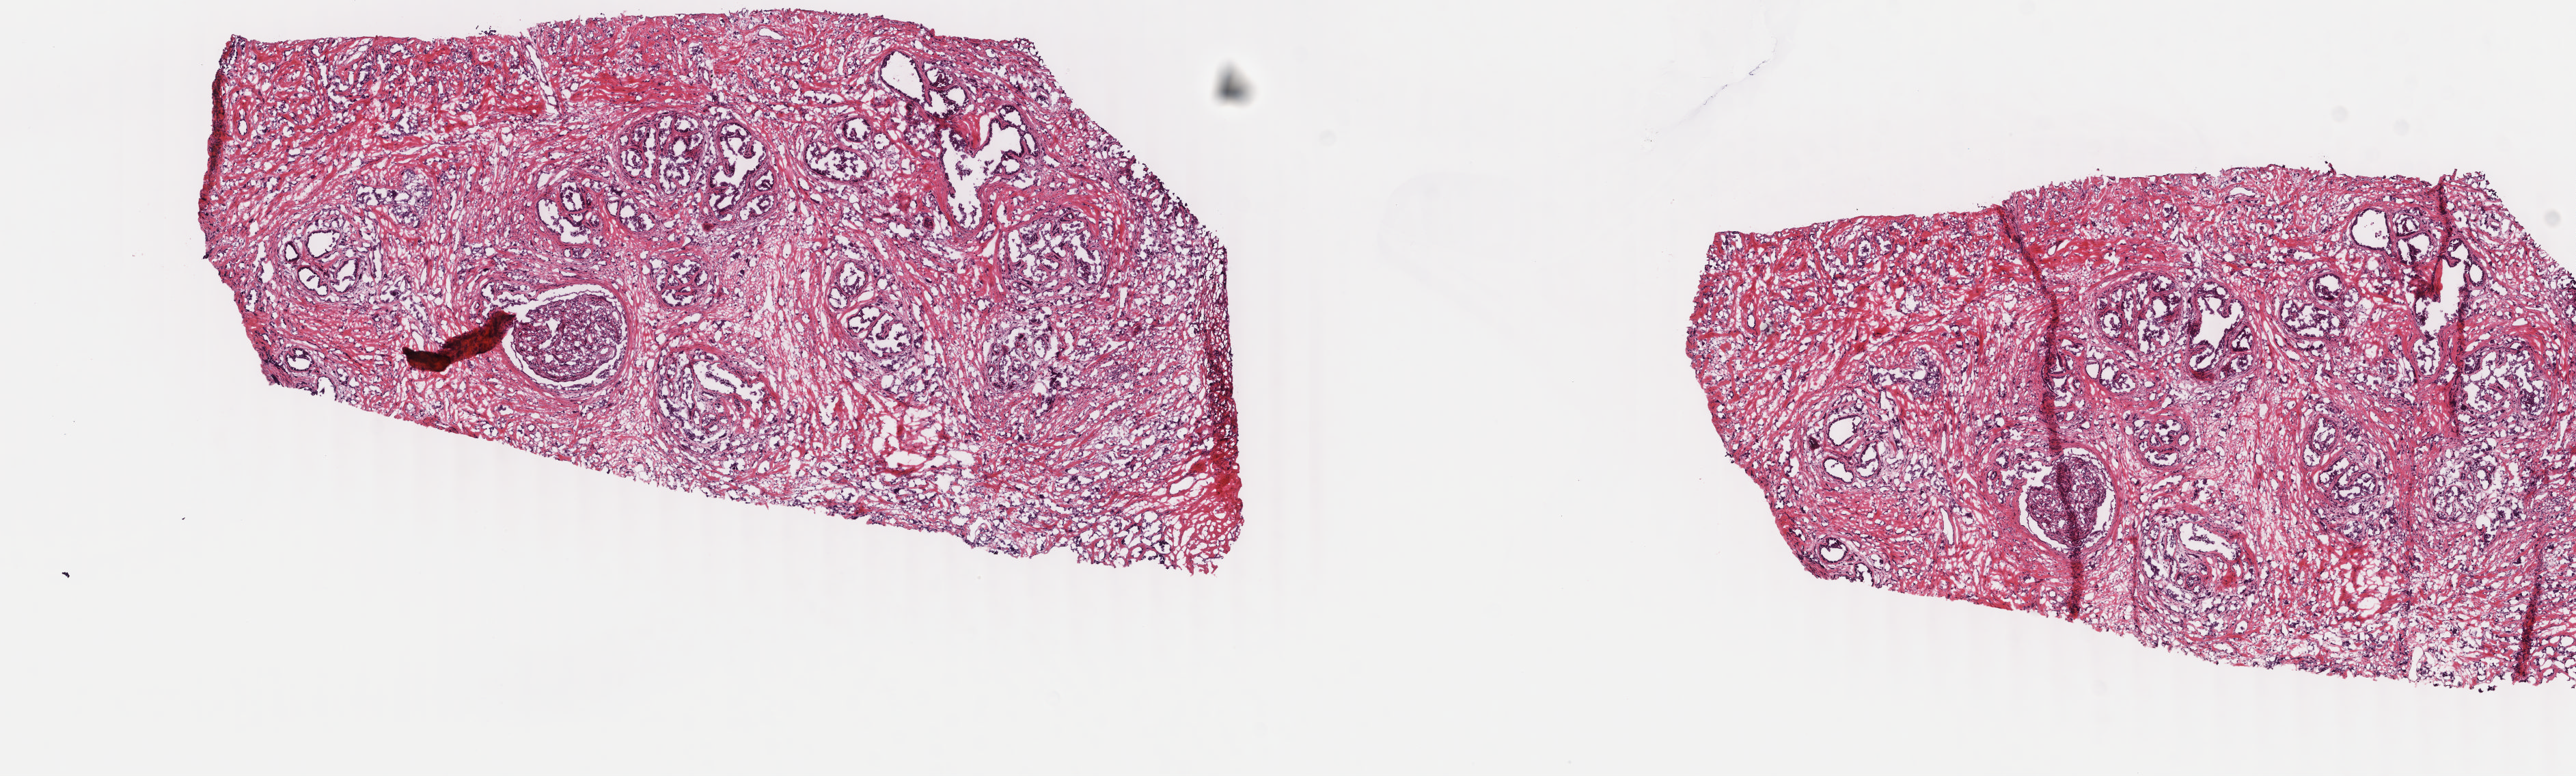
Digitized H&E tissue section (whole slide) — shown as a low-resolution overview of the whole scanned area (about 15.0 x 4.5 mm), frozen section, breast, primary tumour sample. Female patient; age at initial diagnosis 40 years. Pathologist review of this section (percent, as recorded): tumour cells 70%, tumour nuclei 70%.
Histologic diagnosis: Infiltrating duct carcinoma, NOS.